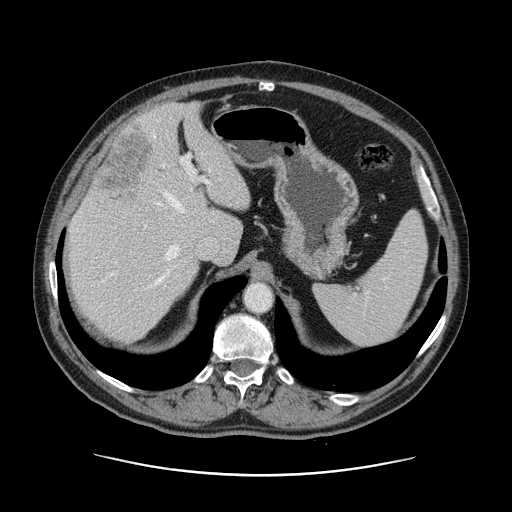
Contrast-enhanced abdominal CT, one axial slice; slice 91 of 141 in the series (ordered by position); soft-tissue window (W 400 / L 40 HU); 512 × 512 image matrix, field of view 395 × 395 mm. Male patient, age 72 years. From the clinical record (not read from this slice): diagnosis: colorectal cancer liver metastases, imaged before liver resection; multiple liver metastases: yes; largest metastasis: 5.4 cm.
Outlined on this slice (manually delineated by an expert):
- hepatic veins: bounding box <155,153,203,286> (left, top, right, bottom; pixels)
- liver: <67,105,250,339>
- planned liver remnant (the part of the liver to remain after resection): <68,104,250,339>
- portal vein (with intrahepatic branches): <101,154,210,282>
- liver metastasis: <98,123,153,206>